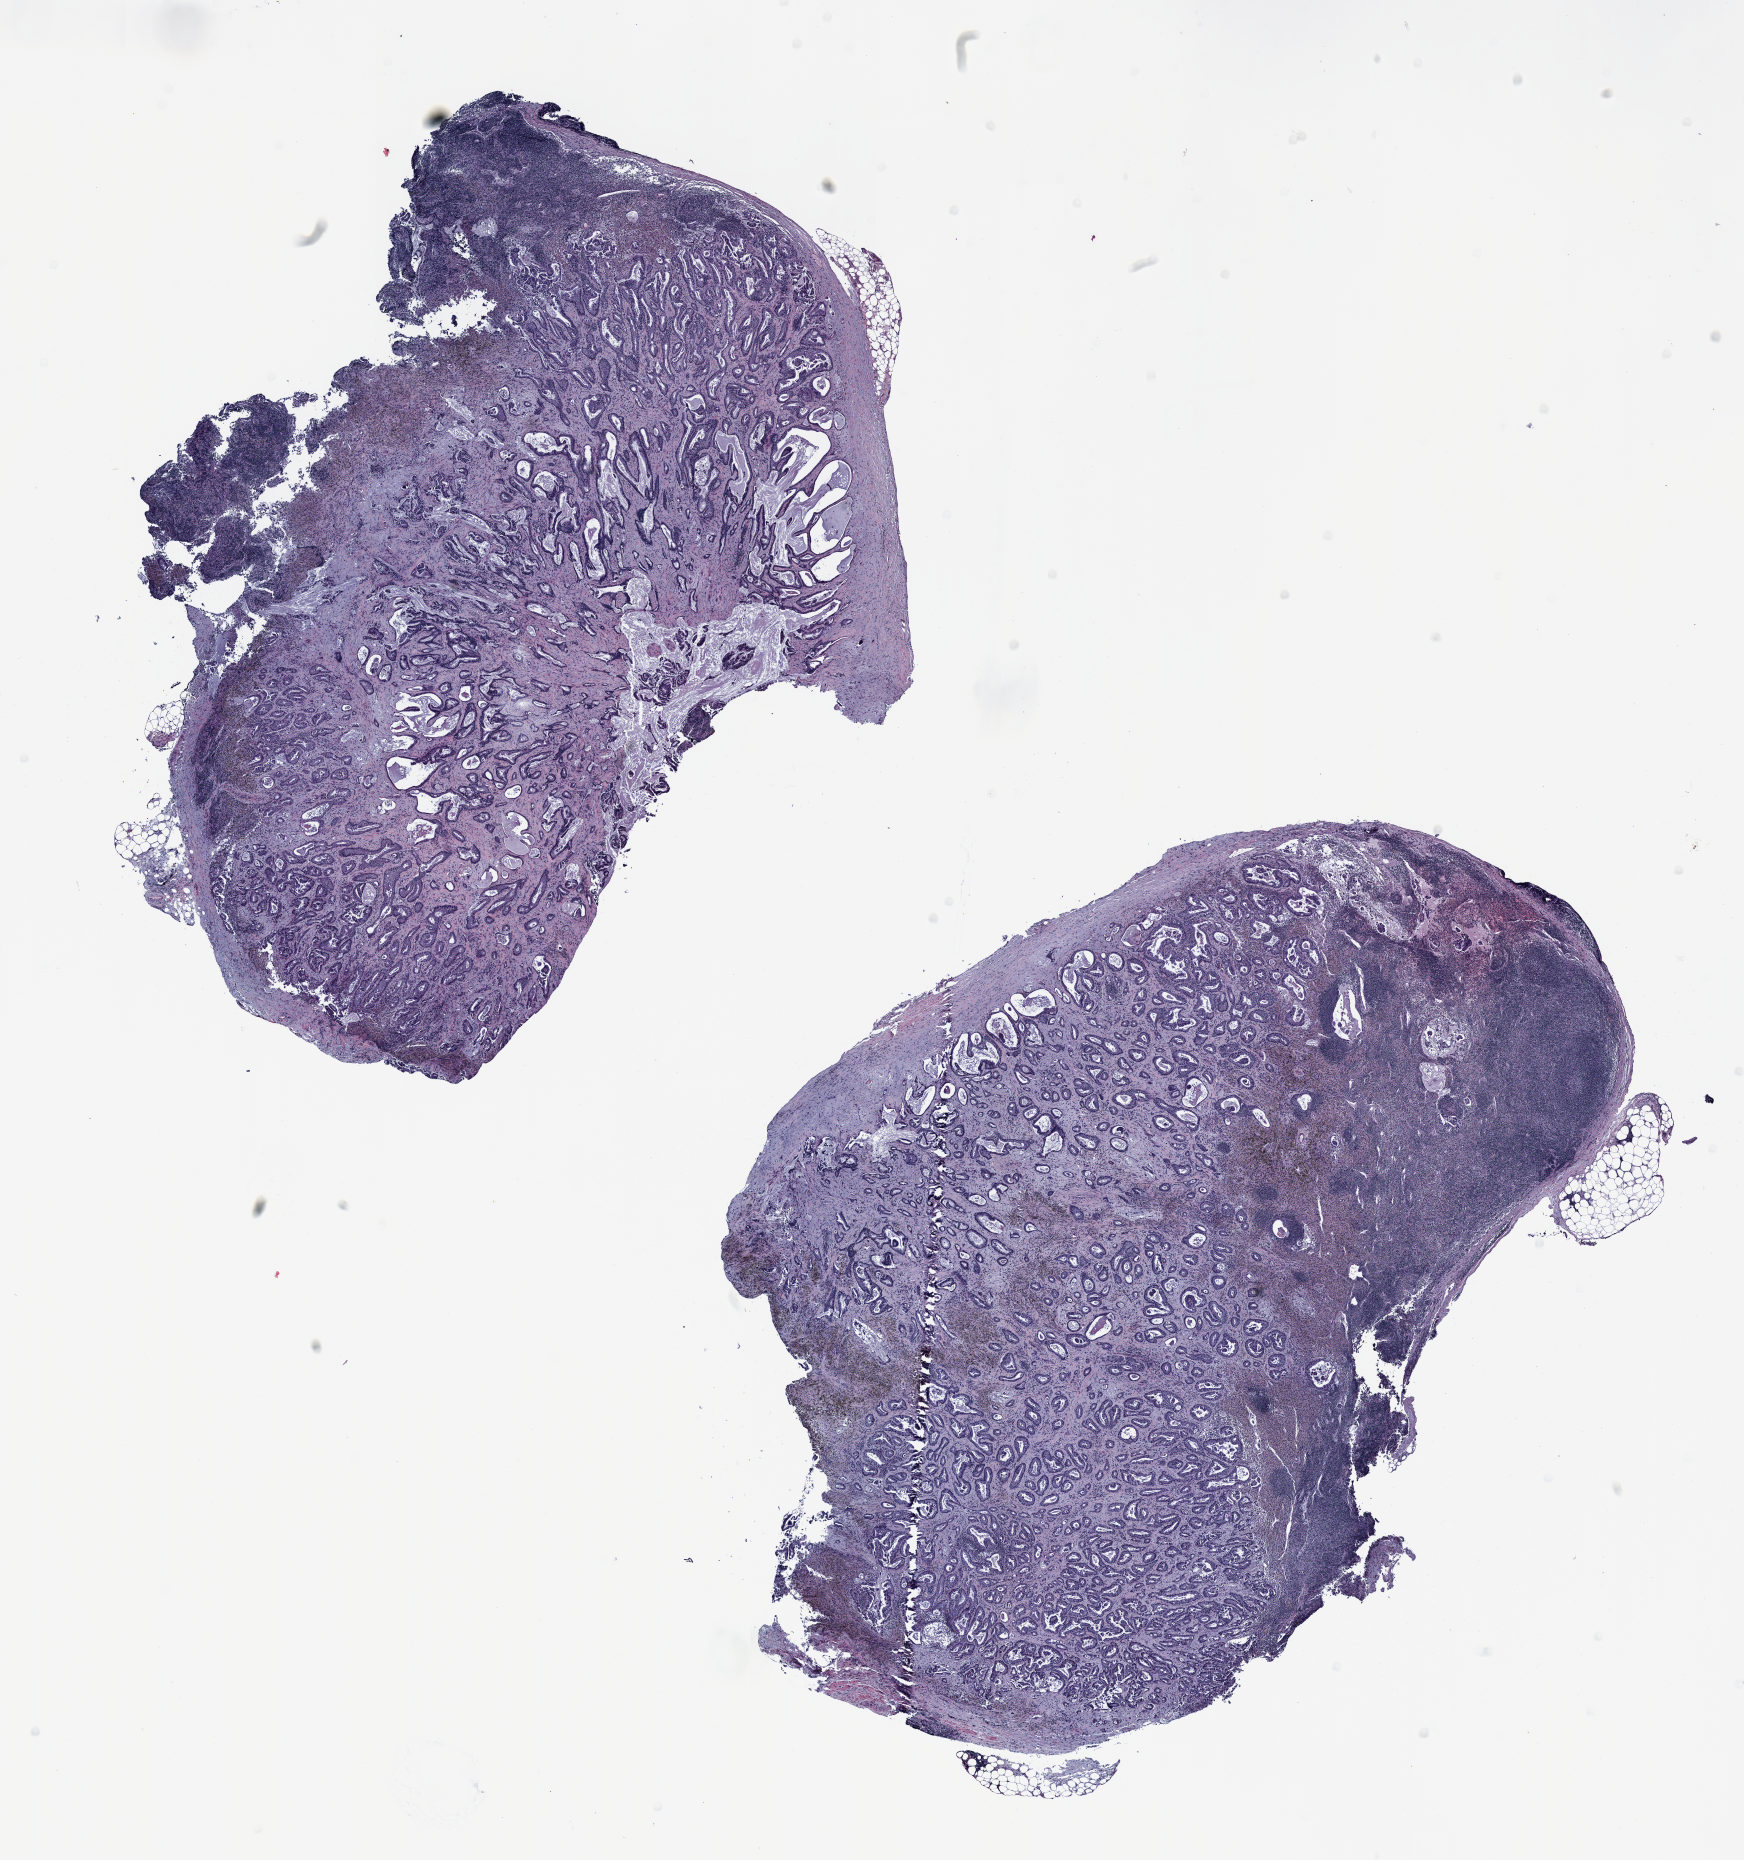
H&E-stained whole-slide image — whole scanned area (about 14.0 x 14.9 mm, from a 20x scan) shown as a low-resolution overview. FFPE section. Lung. Male, age 58 at enrolment. Current smoker at enrolment. Grade: moderately differentiated (G2).
Participant's lung-cancer diagnosis: Adenocarcinoma, NOS (ICD-O-3 8140/3). Stage (AJCC 6th edition): IIA. Primary tumour location (clinical record): right middle lobe. Tumour size (pathology): 10 mm.